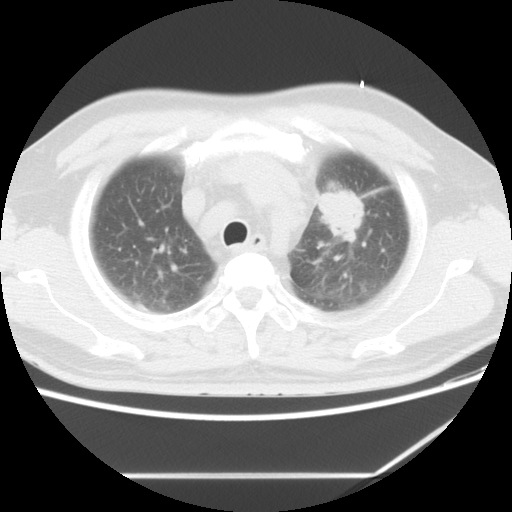
Chest CT, one axial slice; position 9 of 13 along the scan axis; reconstruction kernel STANDARD; lung window (W 1500 / L -600 HU); 5 mm slice thickness; 512 × 512 image matrix, field of view 350 × 350 mm. Patient: male, 56 years. From the clinical record (not read from this slice): clinical TNM (as recorded): T2 N3 M1.
Annotated regions visible in this slice (rectangle marked by the reading radiologist):
- lung tumour (recorded histology: adenocarcinoma): bounding box (x1, y1, x2, y2) in pixels: (315, 180, 370, 243)